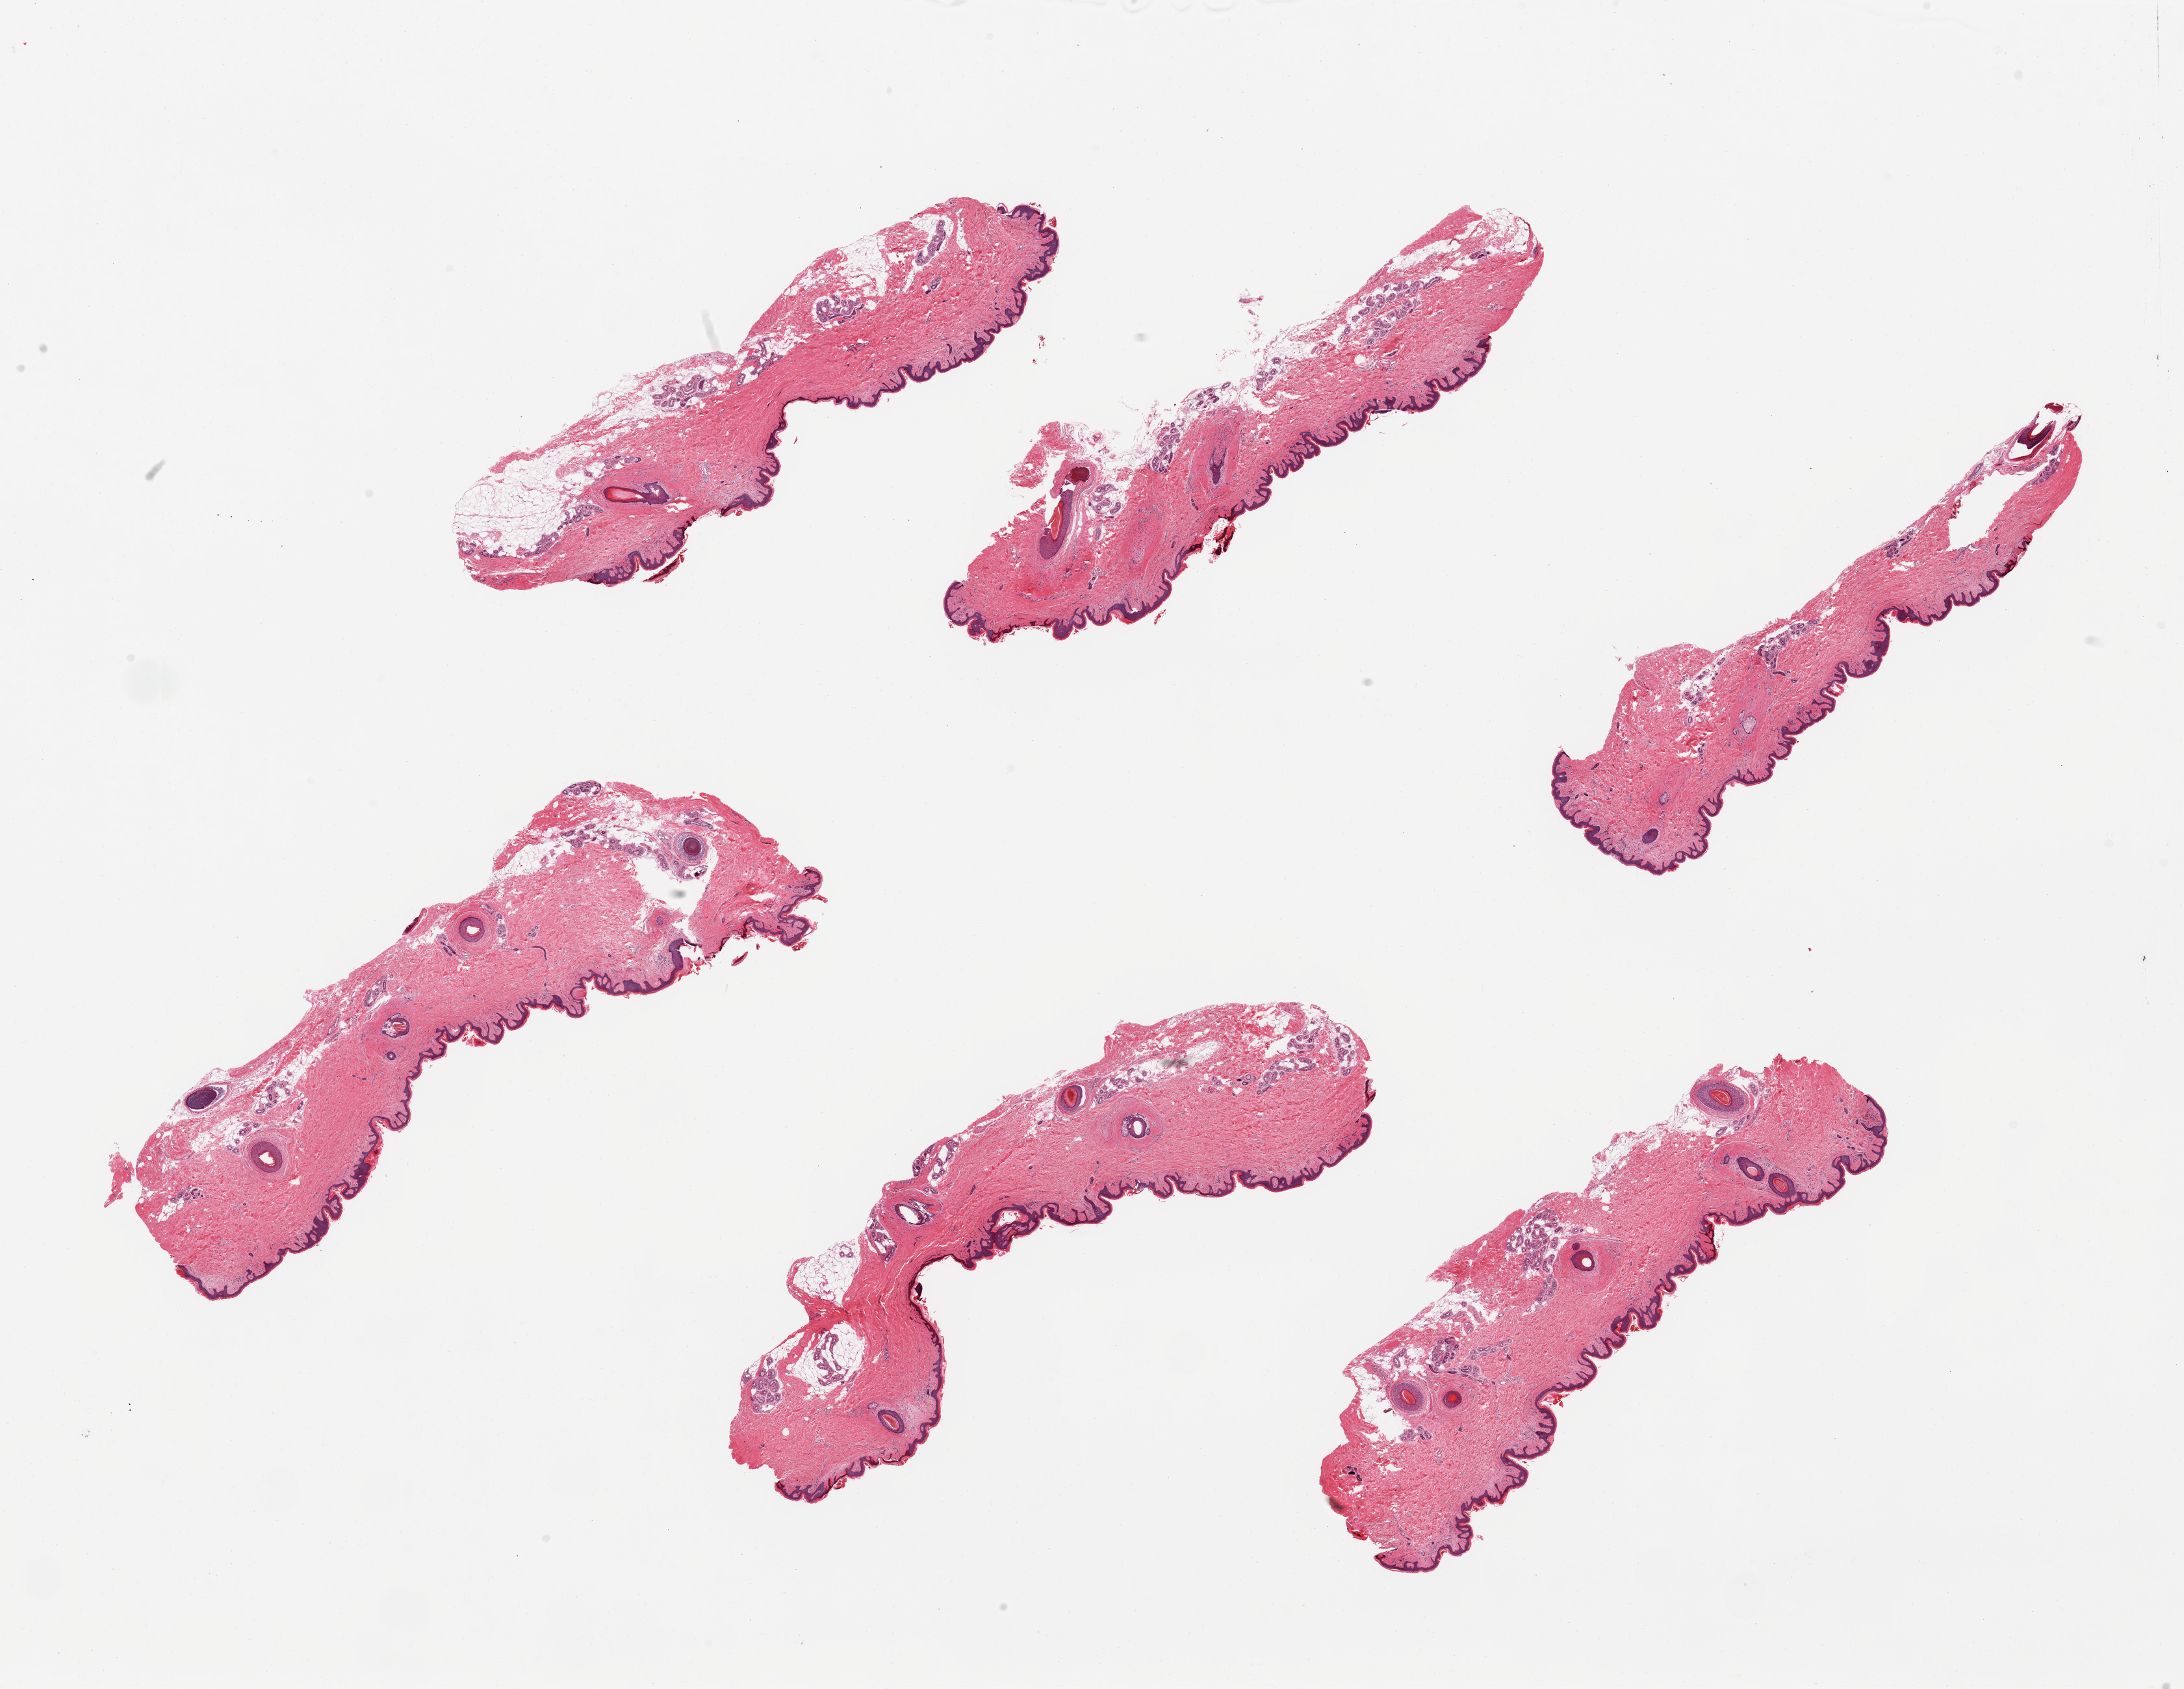
H&E whole-slide image, brightfield — whole scanned area (about 26.6 x 20.6 mm) shown as a low-resolution overview, PAXgene-fixed paraffin-embedded (PFPE) section, section of skin of suprapubic region (target tissue), tissue donor sample. Donor sex: male.
* pathologist's review note for this sample: 6 pieces, squamous epithelium is ~30 microns, trace dermal adherent fat